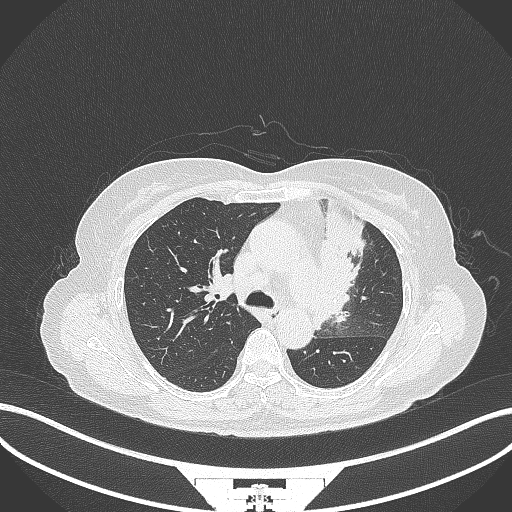
Chest CT, one axial slice. Position 222 of 382 along the scan axis. 120 kVp. Lung window (W 1500 / L -600 HU). 1 mm slice thickness. 512 × 512 image matrix. Female patient, age 64 years. Case-level facts recorded for this patient, not image findings: clinical TNM (as recorded): T2a N2 M0.
Annotated regions visible in this slice (rectangle marked by the reading radiologist):
- lung tumour (recorded histology: adenocarcinoma): bounding box [x1, y1, x2, y2] px = [312, 200, 371, 332]